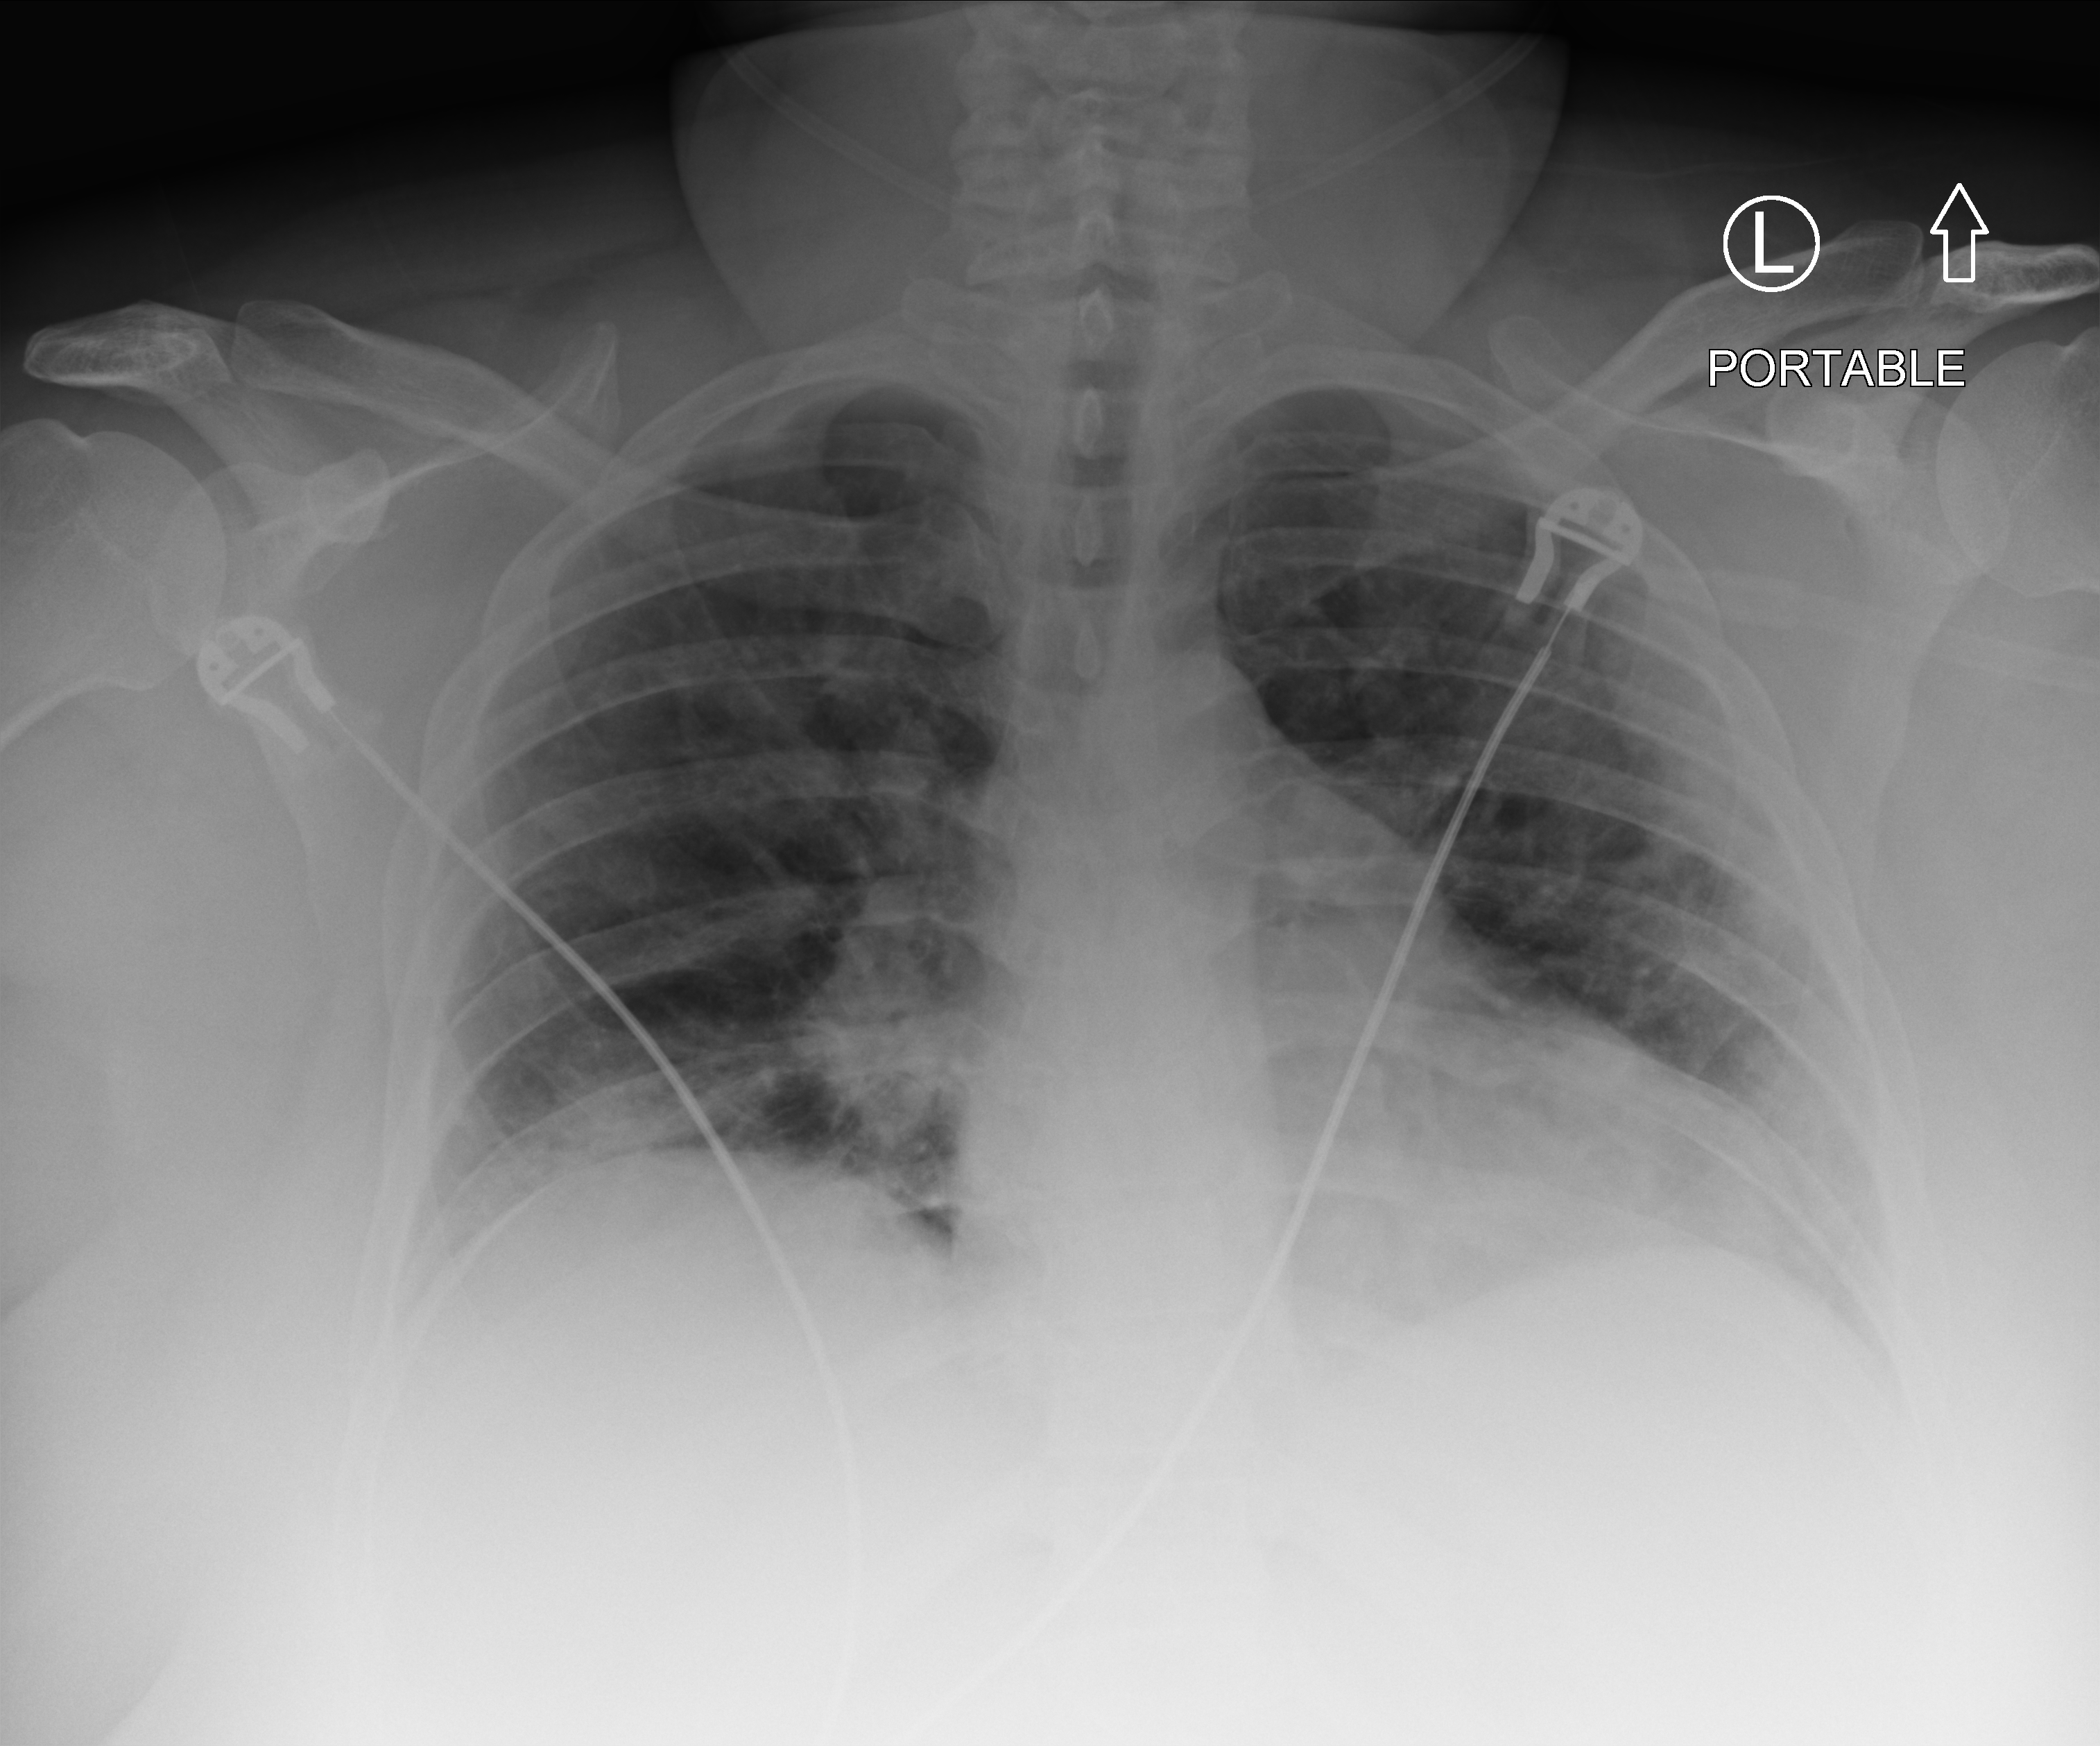
Chest X-ray (portable), anteroposterior (AP) projection. Patient hospitalised with COVID-19; female, aged 18–59 years.
From the hospital-stay record, not from the radiograph (when in the stay this image was taken is not recorded): mechanically ventilated during this hospital stay: no.